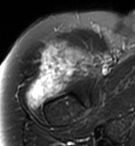
MRI of an extremity soft-tissue mass, one axial slice. Slice 78 of 95 in the series (ordered by position). T2-weighted fat-saturated. MR volume resampled by the dataset authors to the PET/CT grid (not the native acquisition matrix). 3.27 mm slice thickness. 135 × 146 image matrix. Female patient. From the clinical record (not read from this slice): histological type: pleiomorphic undifferentiated sarcoma; grade: high; site of the primary tumour: right quadricep.
Structures marked on this image (expert contour drawn on MRI and transferred to this co-registered scan by the dataset authors):
- gross tumour volume including surrounding oedema: box from (x=26, y=38) to (x=93, y=108) px
- gross tumour volume (mass): (x=39, y=38)–(x=93, y=85)